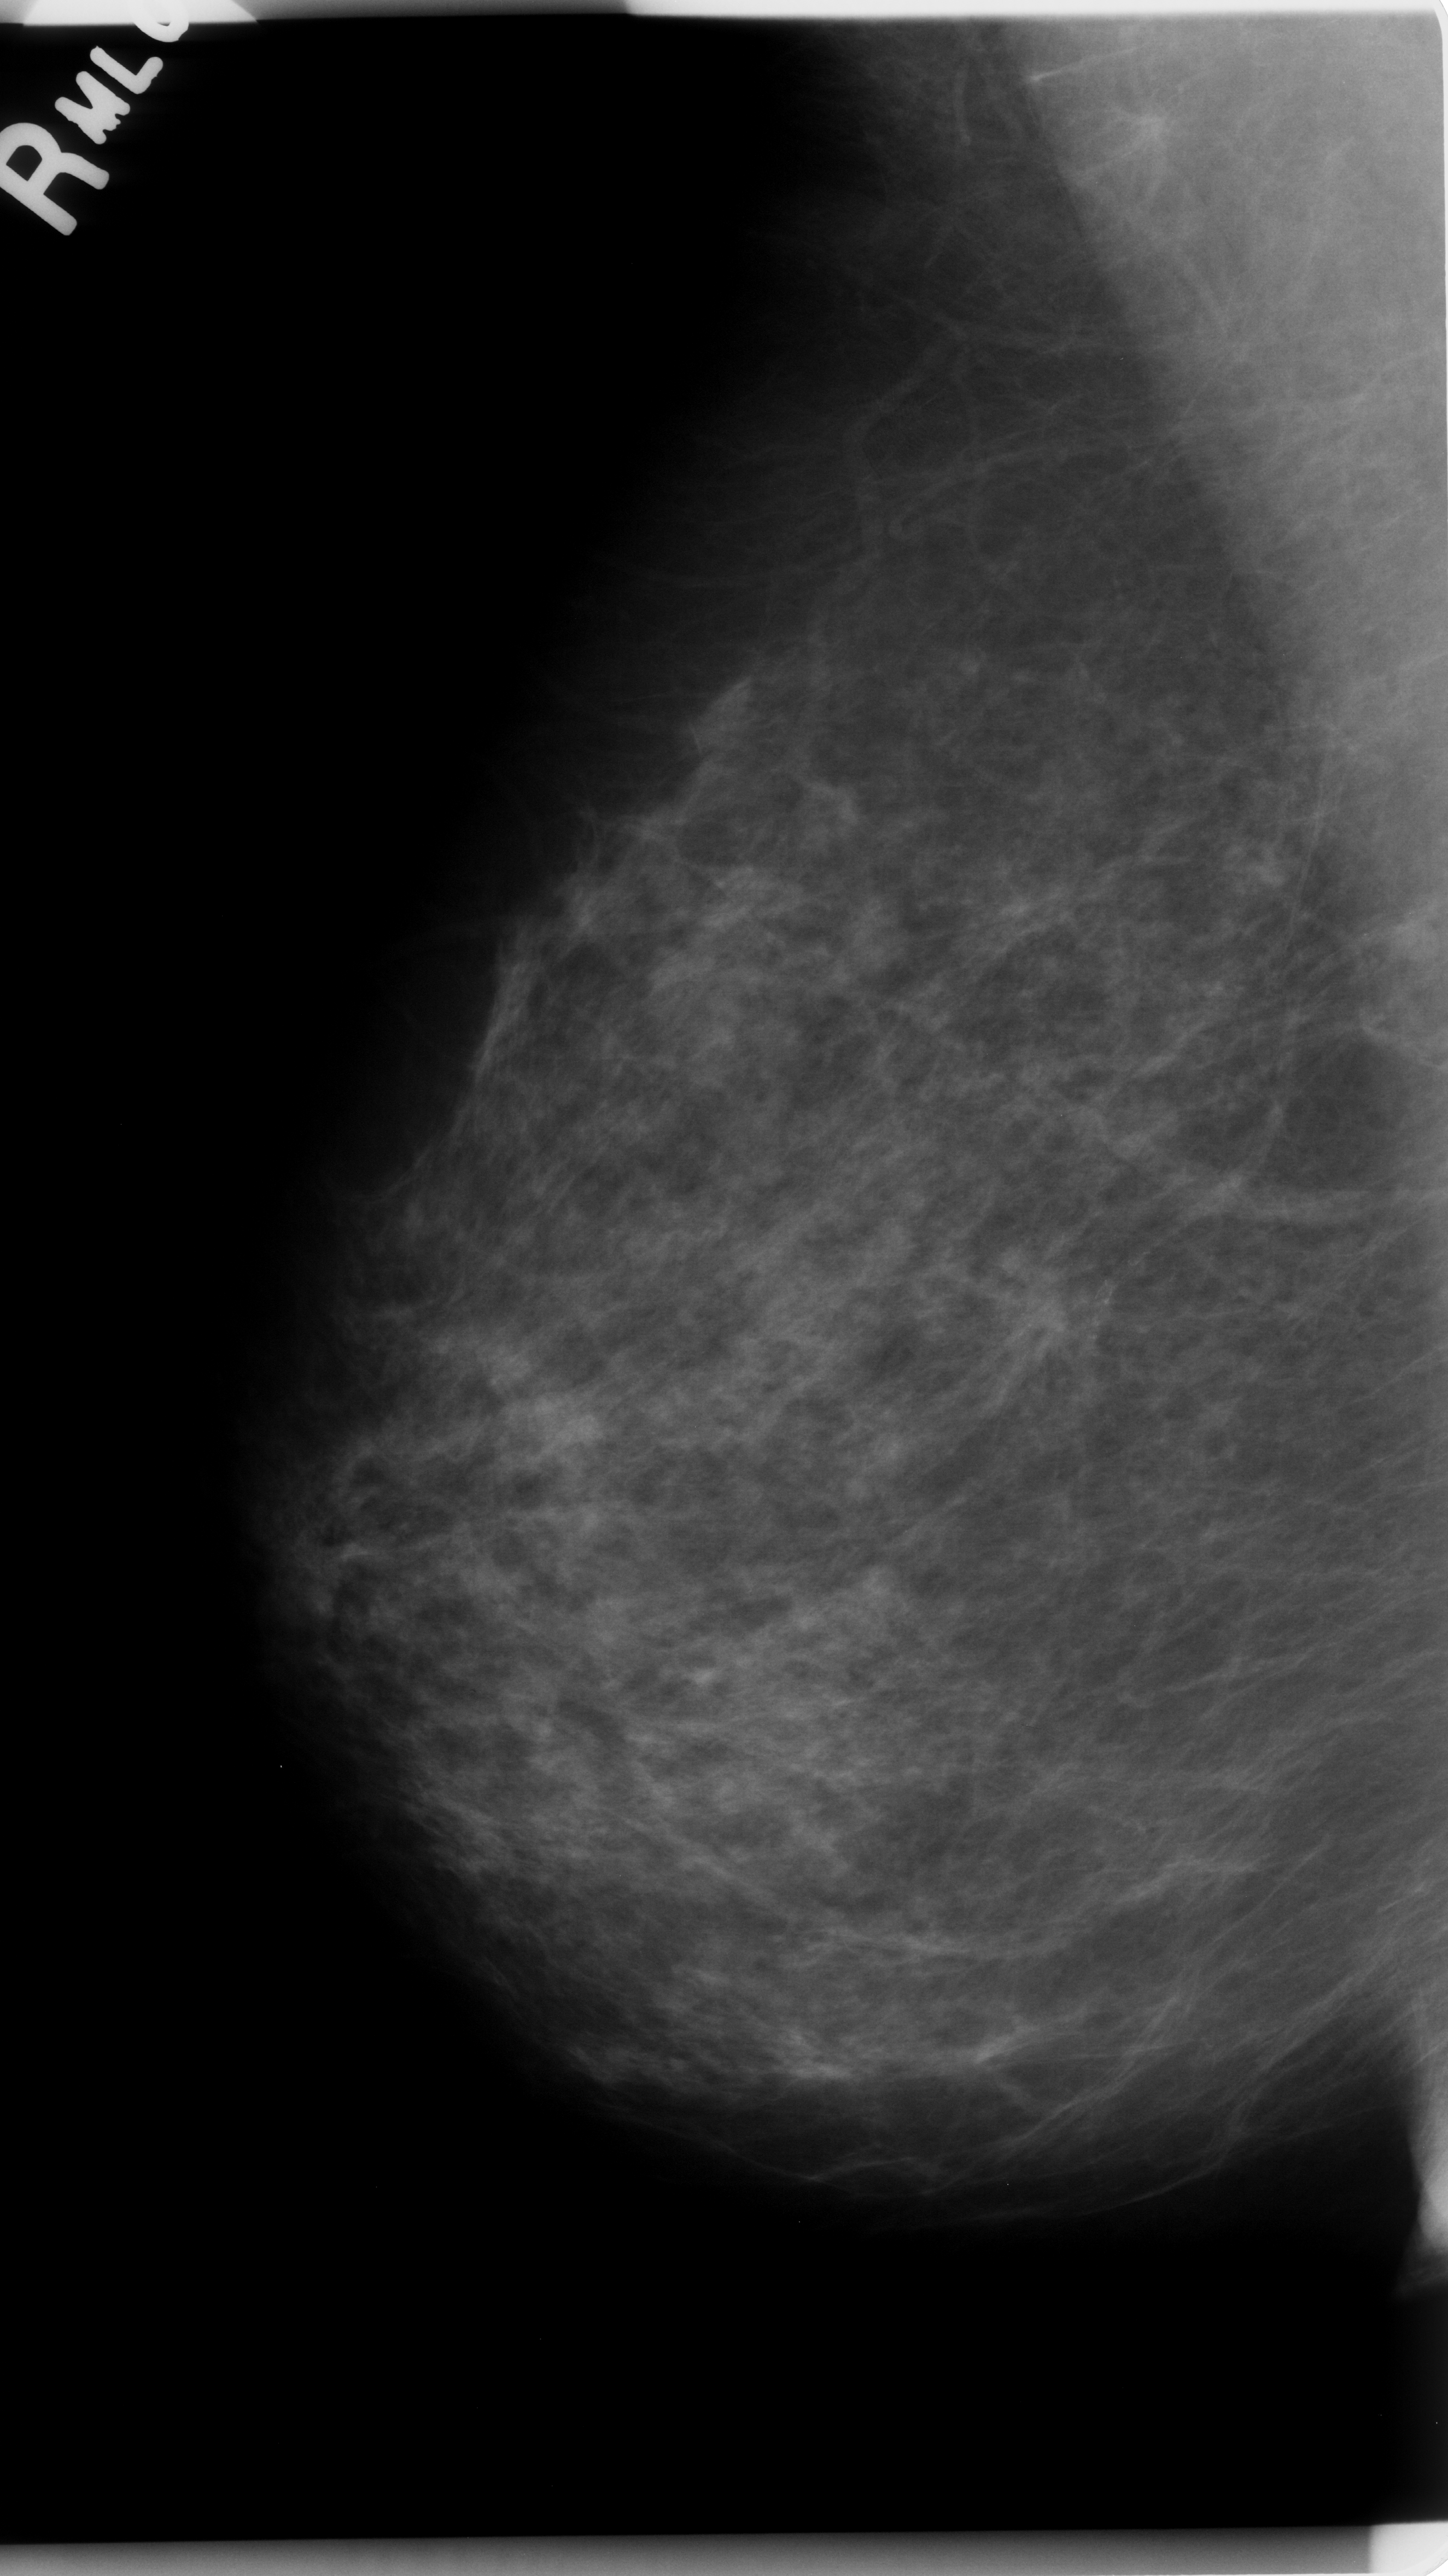
Mammogram (digitized film), right breast, MLO view.
Finding: mass, shape architectural distortion, margins ill defined; BI-RADS assessment category 5; subtlety rating 4 on a 1 (subtle) to 5 (obvious) scale; pathology (as recorded): malignant.